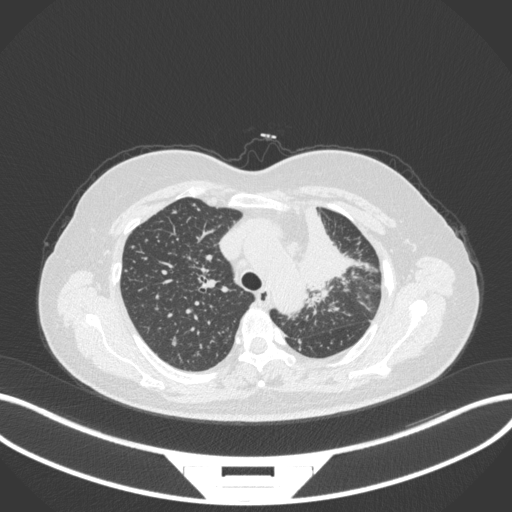
Chest CT, one axial slice. Slice 248 of 348 in the series (ordered by position). 120 kVp. Lung window (W 1500 / L -600 HU). 512 × 512 image matrix. Female patient, age 49 years. From the clinical record (not read from this slice): clinical TNM (as recorded): T1c N0 M1.
Annotated regions visible in this slice (bounding box drawn by a radiologist):
- lung tumour (recorded histology: adenocarcinoma): bounding box (x1, y1, x2, y2) in pixels: (294, 201, 356, 294)